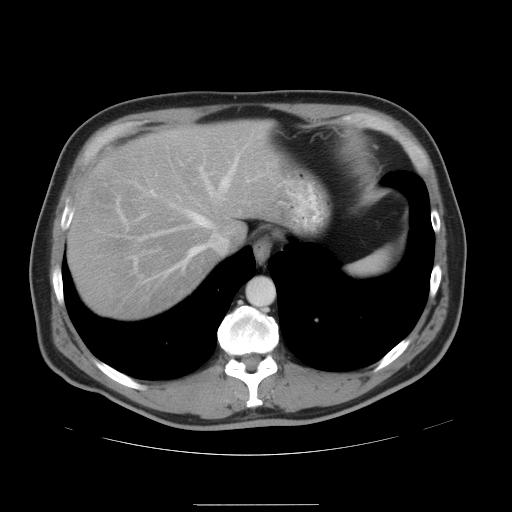
Contrast-enhanced abdominal CT, one axial slice; position 39 of 47 along the scan axis; intravenous contrast given; soft-tissue window (W 400 / L 40 HU); 5 mm slice thickness; 512 × 512 image matrix. Male patient, age 61 years. Case-level facts recorded for this patient, not image findings: diagnosis: colorectal cancer liver metastases, imaged before liver resection; multiple liver metastases: no; largest metastasis: 1.2 cm; disease in both lobes: no.
Annotated regions visible in this slice (outlined manually by an expert reader):
- hepatic veins: bounding box (x1, y1, x2, y2) in pixels: (151, 157, 238, 273)
- liver: (67, 120, 288, 321)
- planned liver remnant (the part of the liver to remain after resection): (67, 120, 288, 321)
- portal vein (with intrahepatic branches): (122, 177, 251, 262)